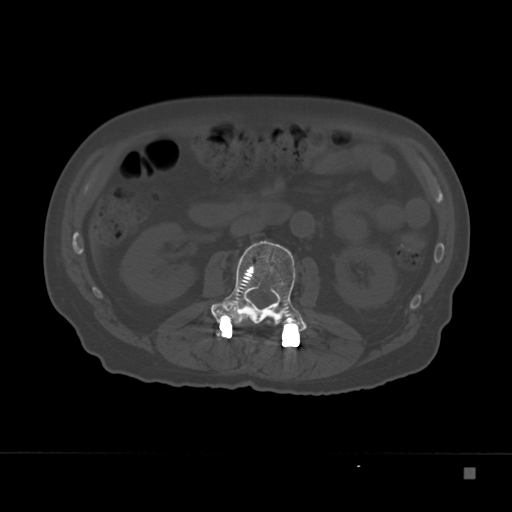
CT including the spine, one axial slice; slice 90 of 332 in the series (ordered by position); 120 kVp; bone window (W 1800 / L 400 HU); 1.5 mm slice thickness; 512 × 512 image matrix, field of view 389 × 389 mm. Male patient, age 72 years. From the clinical record (not read from this slice): primary cancer: skeletal.
Outlined on this slice (semi-automatic segmentation, software-assisted and operator-edited):
- L1 vertebra: bounding box [x1, y1, x2, y2] px = [266, 321, 272, 326]
- L2 vertebra: [211, 240, 307, 331]